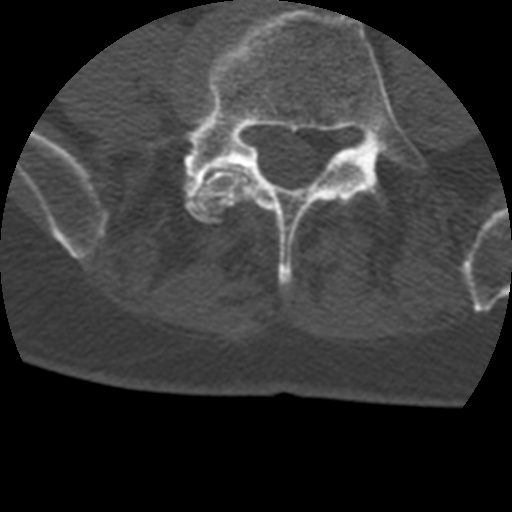
CT including the spine, one axial slice; position 48 of 399 along the scan axis; reconstruction kernel STANDARD; bone window (W 1800 / L 400 HU); 1.25 mm slice thickness; 512 × 512 image matrix, field of view 160 × 160 mm. Patient age 69 years. Case-level facts recorded for this patient, not image findings: primary cancer: prostate.
Structures marked on this image (semi-automatically segmented with operator editing):
- L4 vertebra: bounding box [x1, y1, x2, y2] px = [196, 168, 353, 220]
- L5 vertebra: [138, 9, 426, 288]